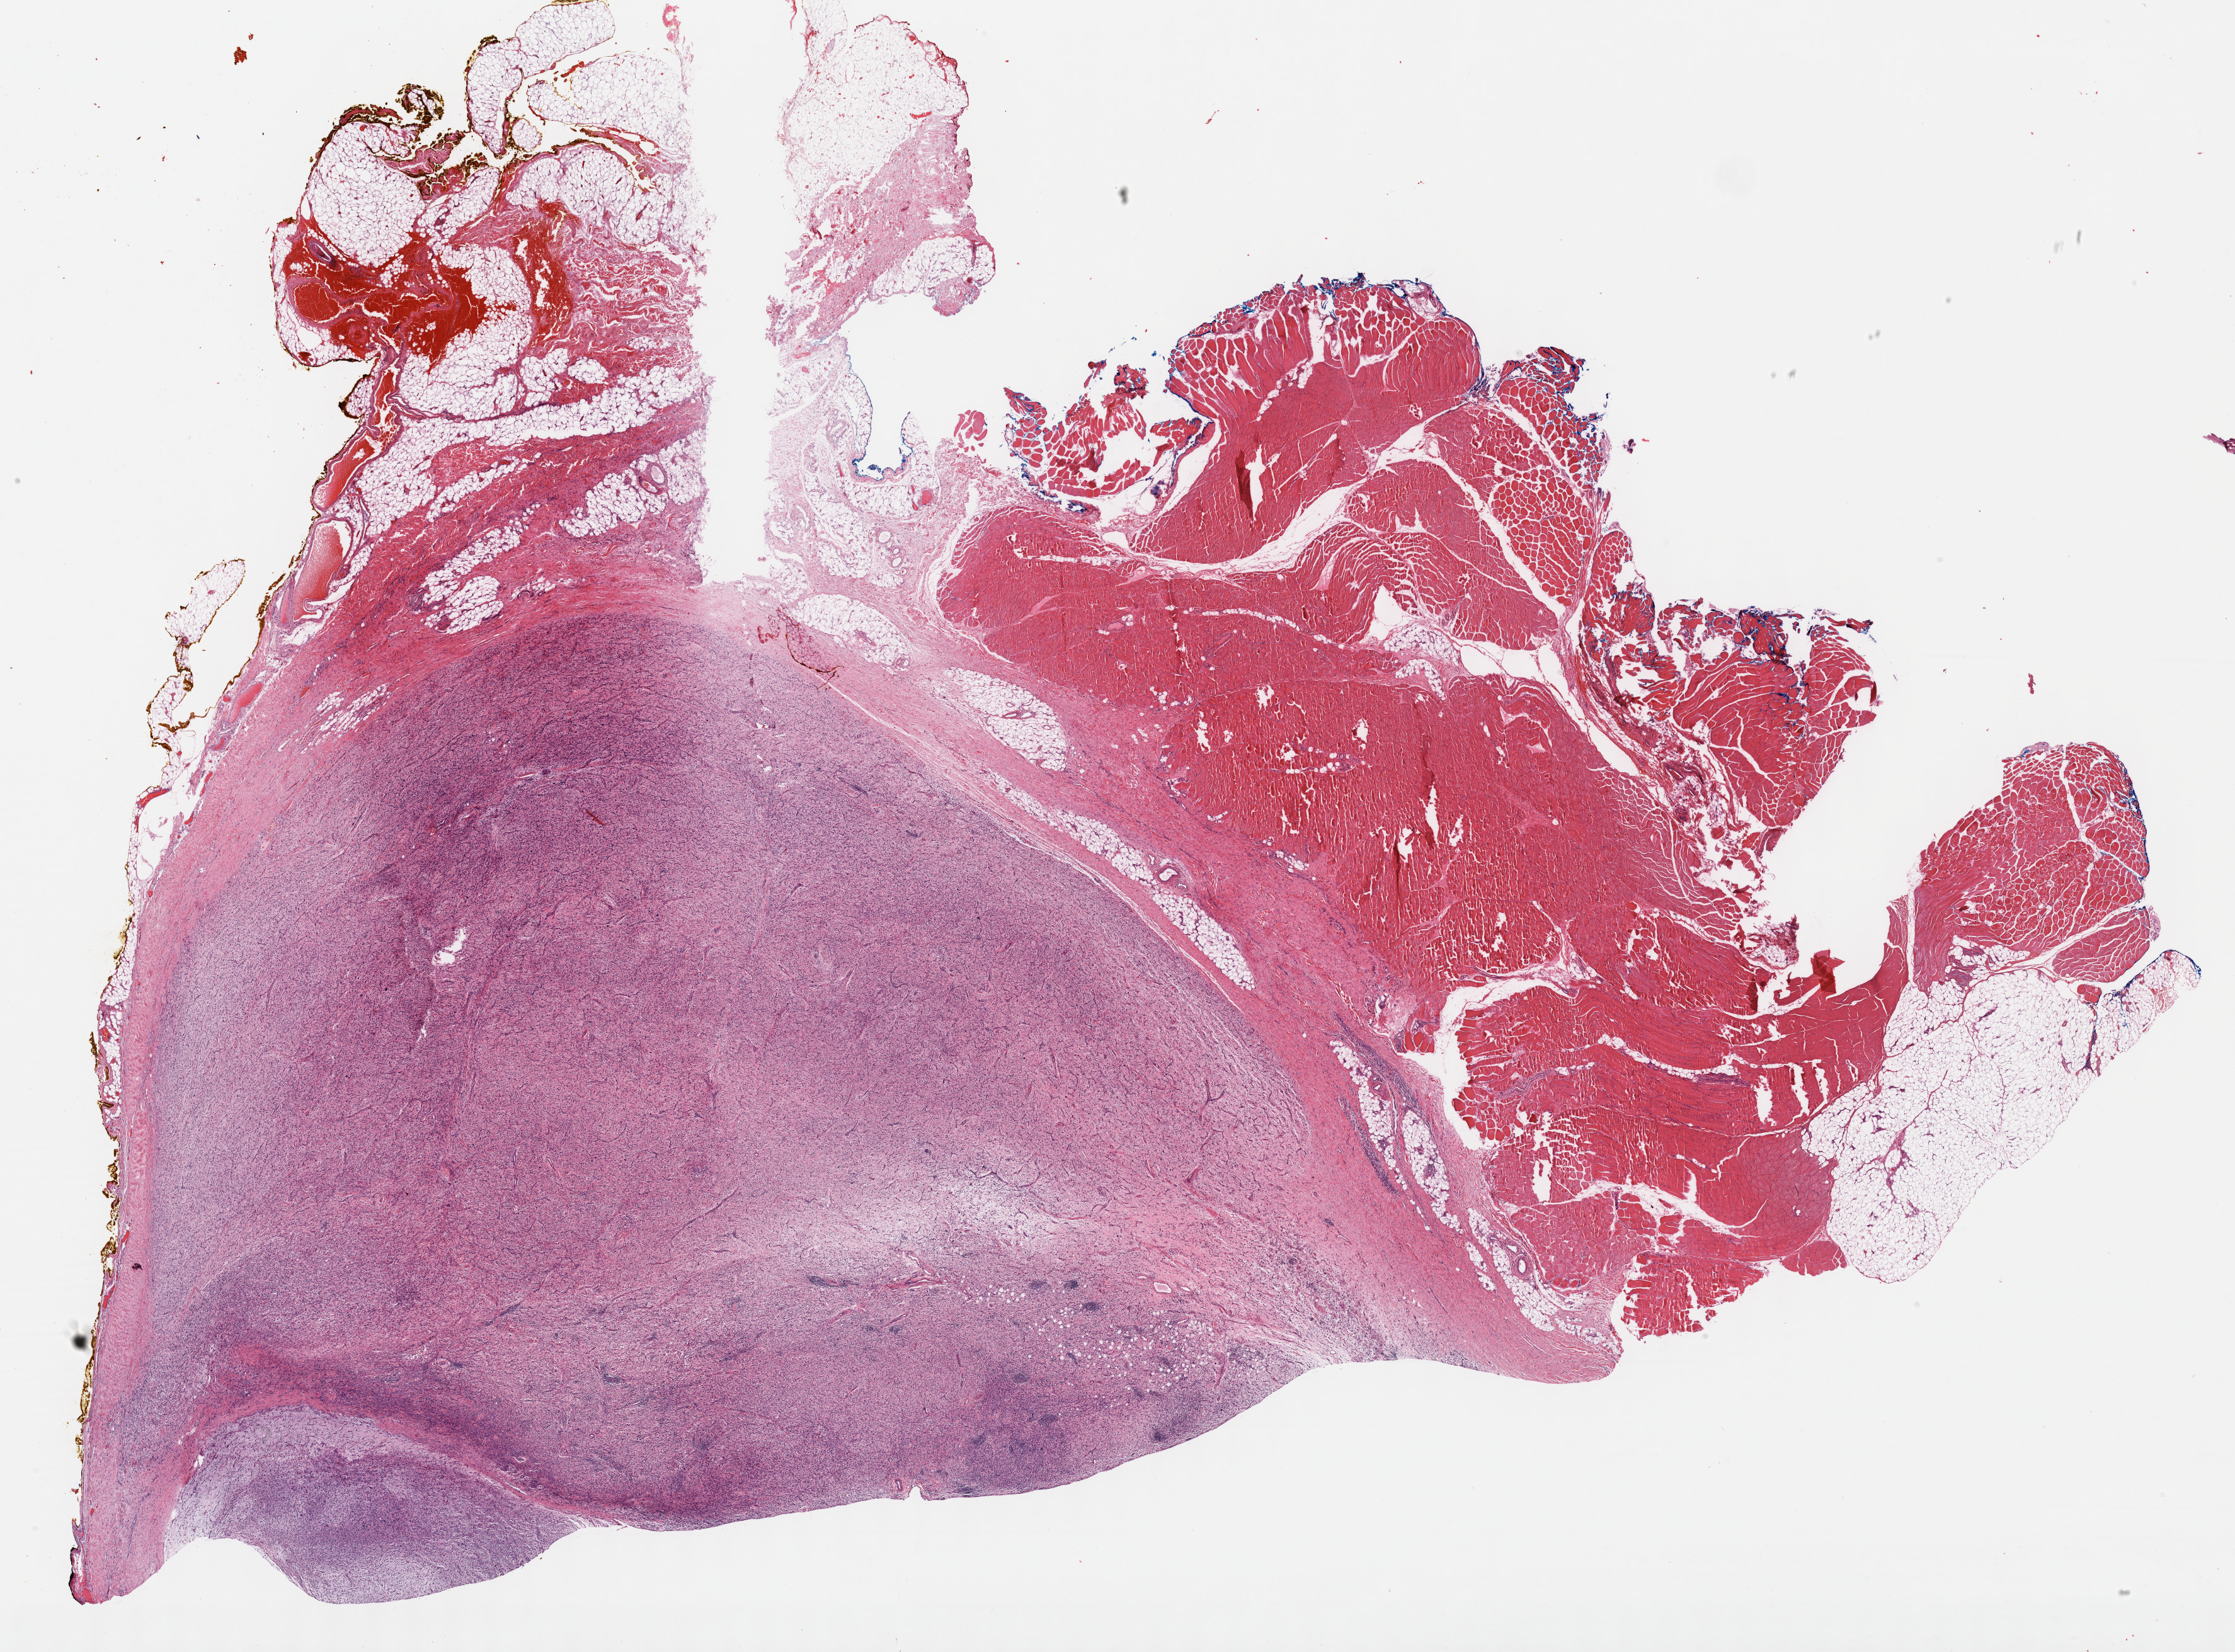
H&E whole-slide image — shown as a low-resolution overview of the whole scanned area (about 28.7 x 21.2 mm, slide scanned at 40x), formalin-fixed paraffin-embedded (FFPE) diagnostic section, sample: primary tumour, connective, subcutaneous and other soft tissues. Male, age 35 years at initial diagnosis.
Histologic diagnosis: Fibromyxosarcoma (connective, subcutaneous and other soft tissues of lower limb and hip).